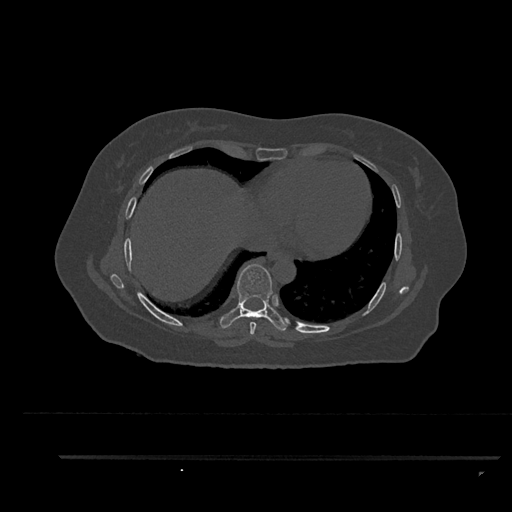
CT including the spine, one axial slice; position 470 of 797 along the scan axis; bone window (W 1800 / L 400 HU); 0.5 mm slice thickness; 512 × 512 image matrix. Female patient, age 44 years. Case-level facts recorded for this patient, not image findings: primary cancer: renal.
Outlined on this slice (semi-automatically segmented with operator editing):
- T7 vertebra: bounding box <250,322,256,335> (left, top, right, bottom; pixels)
- T8 vertebra: <220,264,288,331>